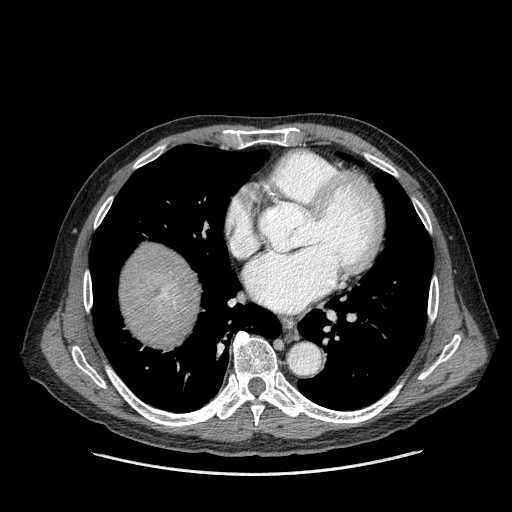
Contrast-enhanced abdominal CT (liver protocol), one axial slice; slice 160 of 180 in the series (ordered by position); reconstruction kernel STANDARD; 120 kVp; one of 2 acquisitions stored at this slice position; soft-tissue window (W 400 / L 40 HU); 2.5 mm slice thickness; 512 × 512 image matrix. Case-level facts recorded for this patient, not image findings: diagnosis: hepatocellular carcinoma (patient treated with transarterial chemoembolisation; whether this scan precedes or follows treatment is not stated here); TNM stage (as recorded): Stage-II; Child-Pugh class: A; tumour differentiation: well differentiated; tumour nodularity: multinodular.
Annotated regions visible in this slice (semi-automatically segmented with operator editing):
- liver parenchyma outside the tumour (the mass and vessels are separate outlines, so this box may not span the whole liver): bounding box (x1, y1, x2, y2) in pixels: (120, 242, 200, 346)
- mass: (139, 275, 167, 305)